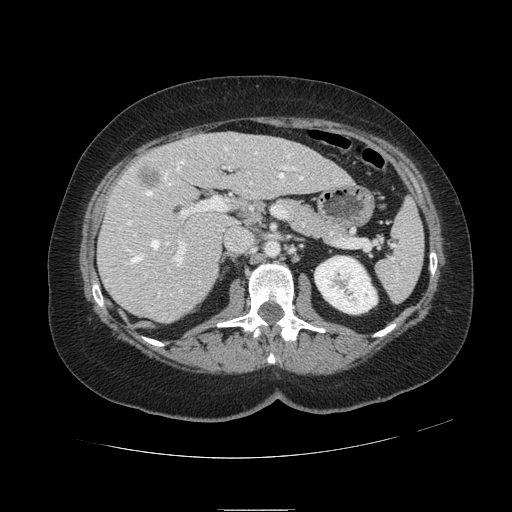
Contrast-enhanced abdominal CT, one axial slice; slice 57 of 121 in the series (ordered by position); intravenous contrast given; soft-tissue window (W 400 / L 40 HU); 2.5 mm slice thickness; 512 × 512 image matrix. Female patient, age 52 years. From the clinical record (not read from this slice): diagnosis: colorectal cancer liver metastases, imaged before liver resection; multiple liver metastases: yes; largest metastasis: 6.3 cm; chemotherapy before resection: yes.
Annotated regions visible in this slice (manually delineated by an expert):
- hepatic veins: bounding box <126,147,303,292> (left, top, right, bottom; pixels)
- liver: <99,132,350,322>
- planned liver remnant (the part of the liver to remain after resection): <168,132,350,199>
- portal vein (with intrahepatic branches): <128,166,296,264>
- liver metastasis: <141,170,159,186>